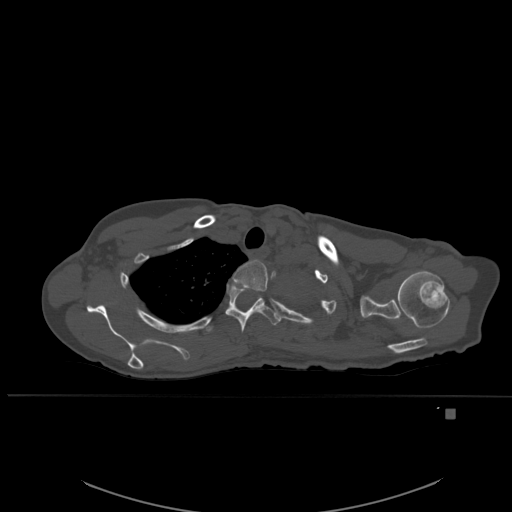
CT including the spine, one axial slice. Bone window (W 1800 / L 400 HU). 512 × 512 image matrix, field of view 440 × 440 mm. Patient: female, 45 years. From the clinical record (not read from this slice): primary cancer: lung.
Structures marked on this image (semi-automatic segmentation, software-assisted and operator-edited):
- T2 vertebra: box from (x=233, y=260) to (x=268, y=292) px
- T3 vertebra: (x=225, y=282)–(x=281, y=333)
- T4 vertebra: (x=205, y=325)–(x=213, y=333)